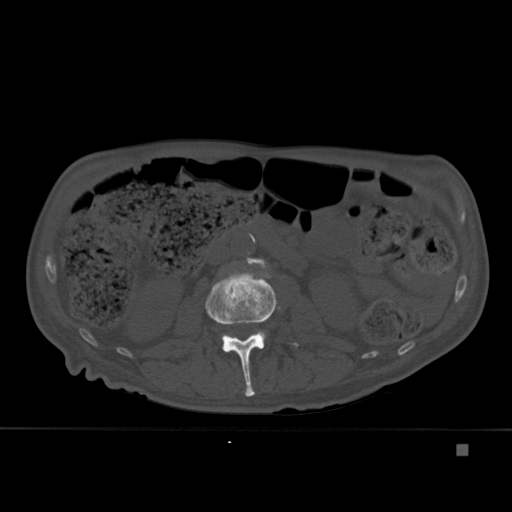
CT including the spine, one axial slice. Slice 158 of 451 in the series (ordered by position). Bone window (W 1800 / L 400 HU). 1.5 mm slice thickness. 512 × 512 image matrix, field of view 378 × 378 mm. Male patient, age 75 years. Case-level facts recorded for this patient, not image findings: primary cancer: prostate.
Outlined on this slice (semi-automatic segmentation, software-assisted and operator-edited):
- L2 vertebra: bounding box [x1, y1, x2, y2] px = [205, 271, 299, 397]
- L3 vertebra: [246, 258, 271, 278]